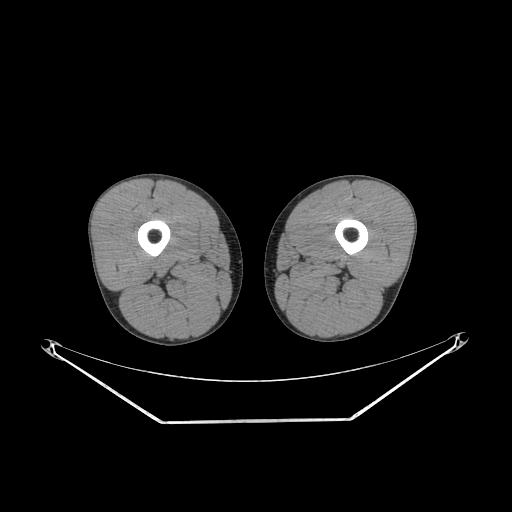
CT of an extremity soft-tissue mass (from a PET/CT study), one axial slice. Slice 212 of 267 in the series (ordered by position). 140 kVp. Soft-tissue window (W 400 / L 40 HU). 3.75 mm slice thickness. 512 × 512 image matrix, field of view 500 × 500 mm. Male patient. Case-level facts recorded for this patient, not image findings: histological type: extraskeletal osteosarcoma; grade: high; site of the primary tumour: left adductur.
Structures marked on this image (expert contour drawn on MRI and transferred to this co-registered scan by the dataset authors):
- gross tumour volume (mass): bounding box [x1, y1, x2, y2] px = [331, 256, 348, 268]